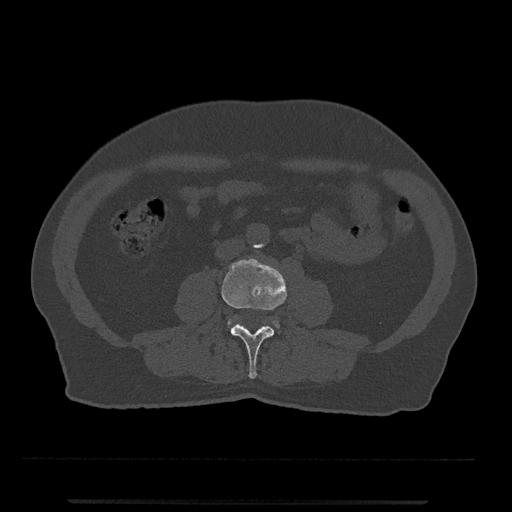
CT including the spine, one axial slice. Slice 186 of 797 in the series (ordered by position). Reconstruction kernel Br40s/3. 120 kVp. Bone window (W 1800 / L 400 HU). 0.5 mm slice thickness. 512 × 512 image matrix, field of view 419 × 419 mm. Male patient, age 63 years. Case-level facts recorded for this patient, not image findings: primary cancer: prostate.
Annotated regions visible in this slice (semi-automatically segmented with operator editing):
- L3 vertebra: bounding box <222,258,287,379> (left, top, right, bottom; pixels)
- L4 vertebra: <227,318,280,329>